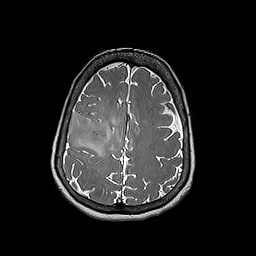
Brain MRI from a brain-tumour surgery series, one axial slice; position 66 of 192 along the scan axis; 256 × 256 image matrix, field of view 250 × 250 mm. From the clinical record (not read from this slice): histopathology: Oligodendroglioma; WHO grade: 3; IDH mutation: yes.
Structures marked on this image (manually delineated by an expert):
- tumour: bounding box (x1, y1, x2, y2) in pixels: (67, 111, 108, 148)